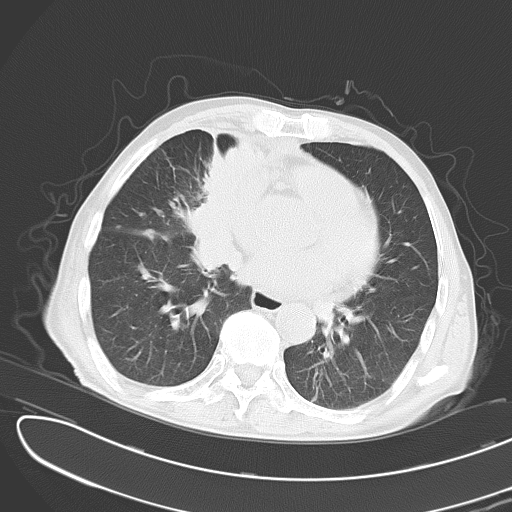
Chest CT, one axial slice. Slice 12 of 43 in the series (ordered by position). 120 kVp. Lung window (W 1500 / L -600 HU). 5 mm slice thickness. 512 × 512 image matrix, field of view 353 × 353 mm. Patient: male, 65 years. From the clinical record (not read from this slice): clinical TNM (as recorded): T2 N3 M1; histopathological grade: G3.
Annotated regions visible in this slice (rectangle marked by the reading radiologist):
- lung tumour (recorded histology: small cell carcinoma): bounding box (x1, y1, x2, y2) in pixels: (163, 109, 278, 284)